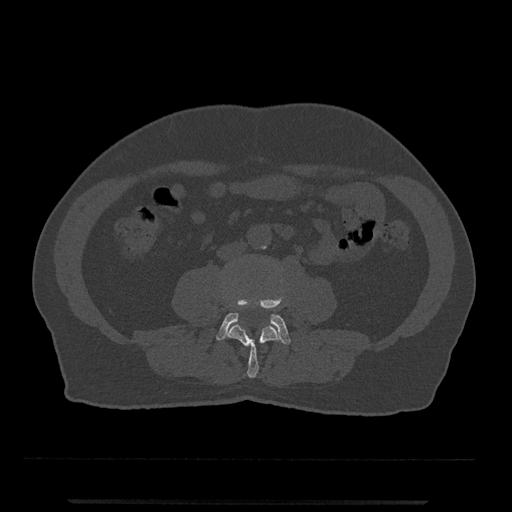
CT including the spine, one axial slice. Position 170 of 797 along the scan axis. 120 kVp. Bone window (W 1800 / L 400 HU). 0.5 mm slice thickness. 512 × 512 image matrix, field of view 419 × 419 mm. Male patient, age 63 years. From the clinical record (not read from this slice): primary cancer: prostate.
Annotated regions visible in this slice (semi-automatic segmentation, software-assisted and operator-edited):
- L3 vertebra: bounding box (x1, y1, x2, y2) in pixels: (221, 295, 281, 378)
- L4 vertebra: (216, 299, 291, 345)